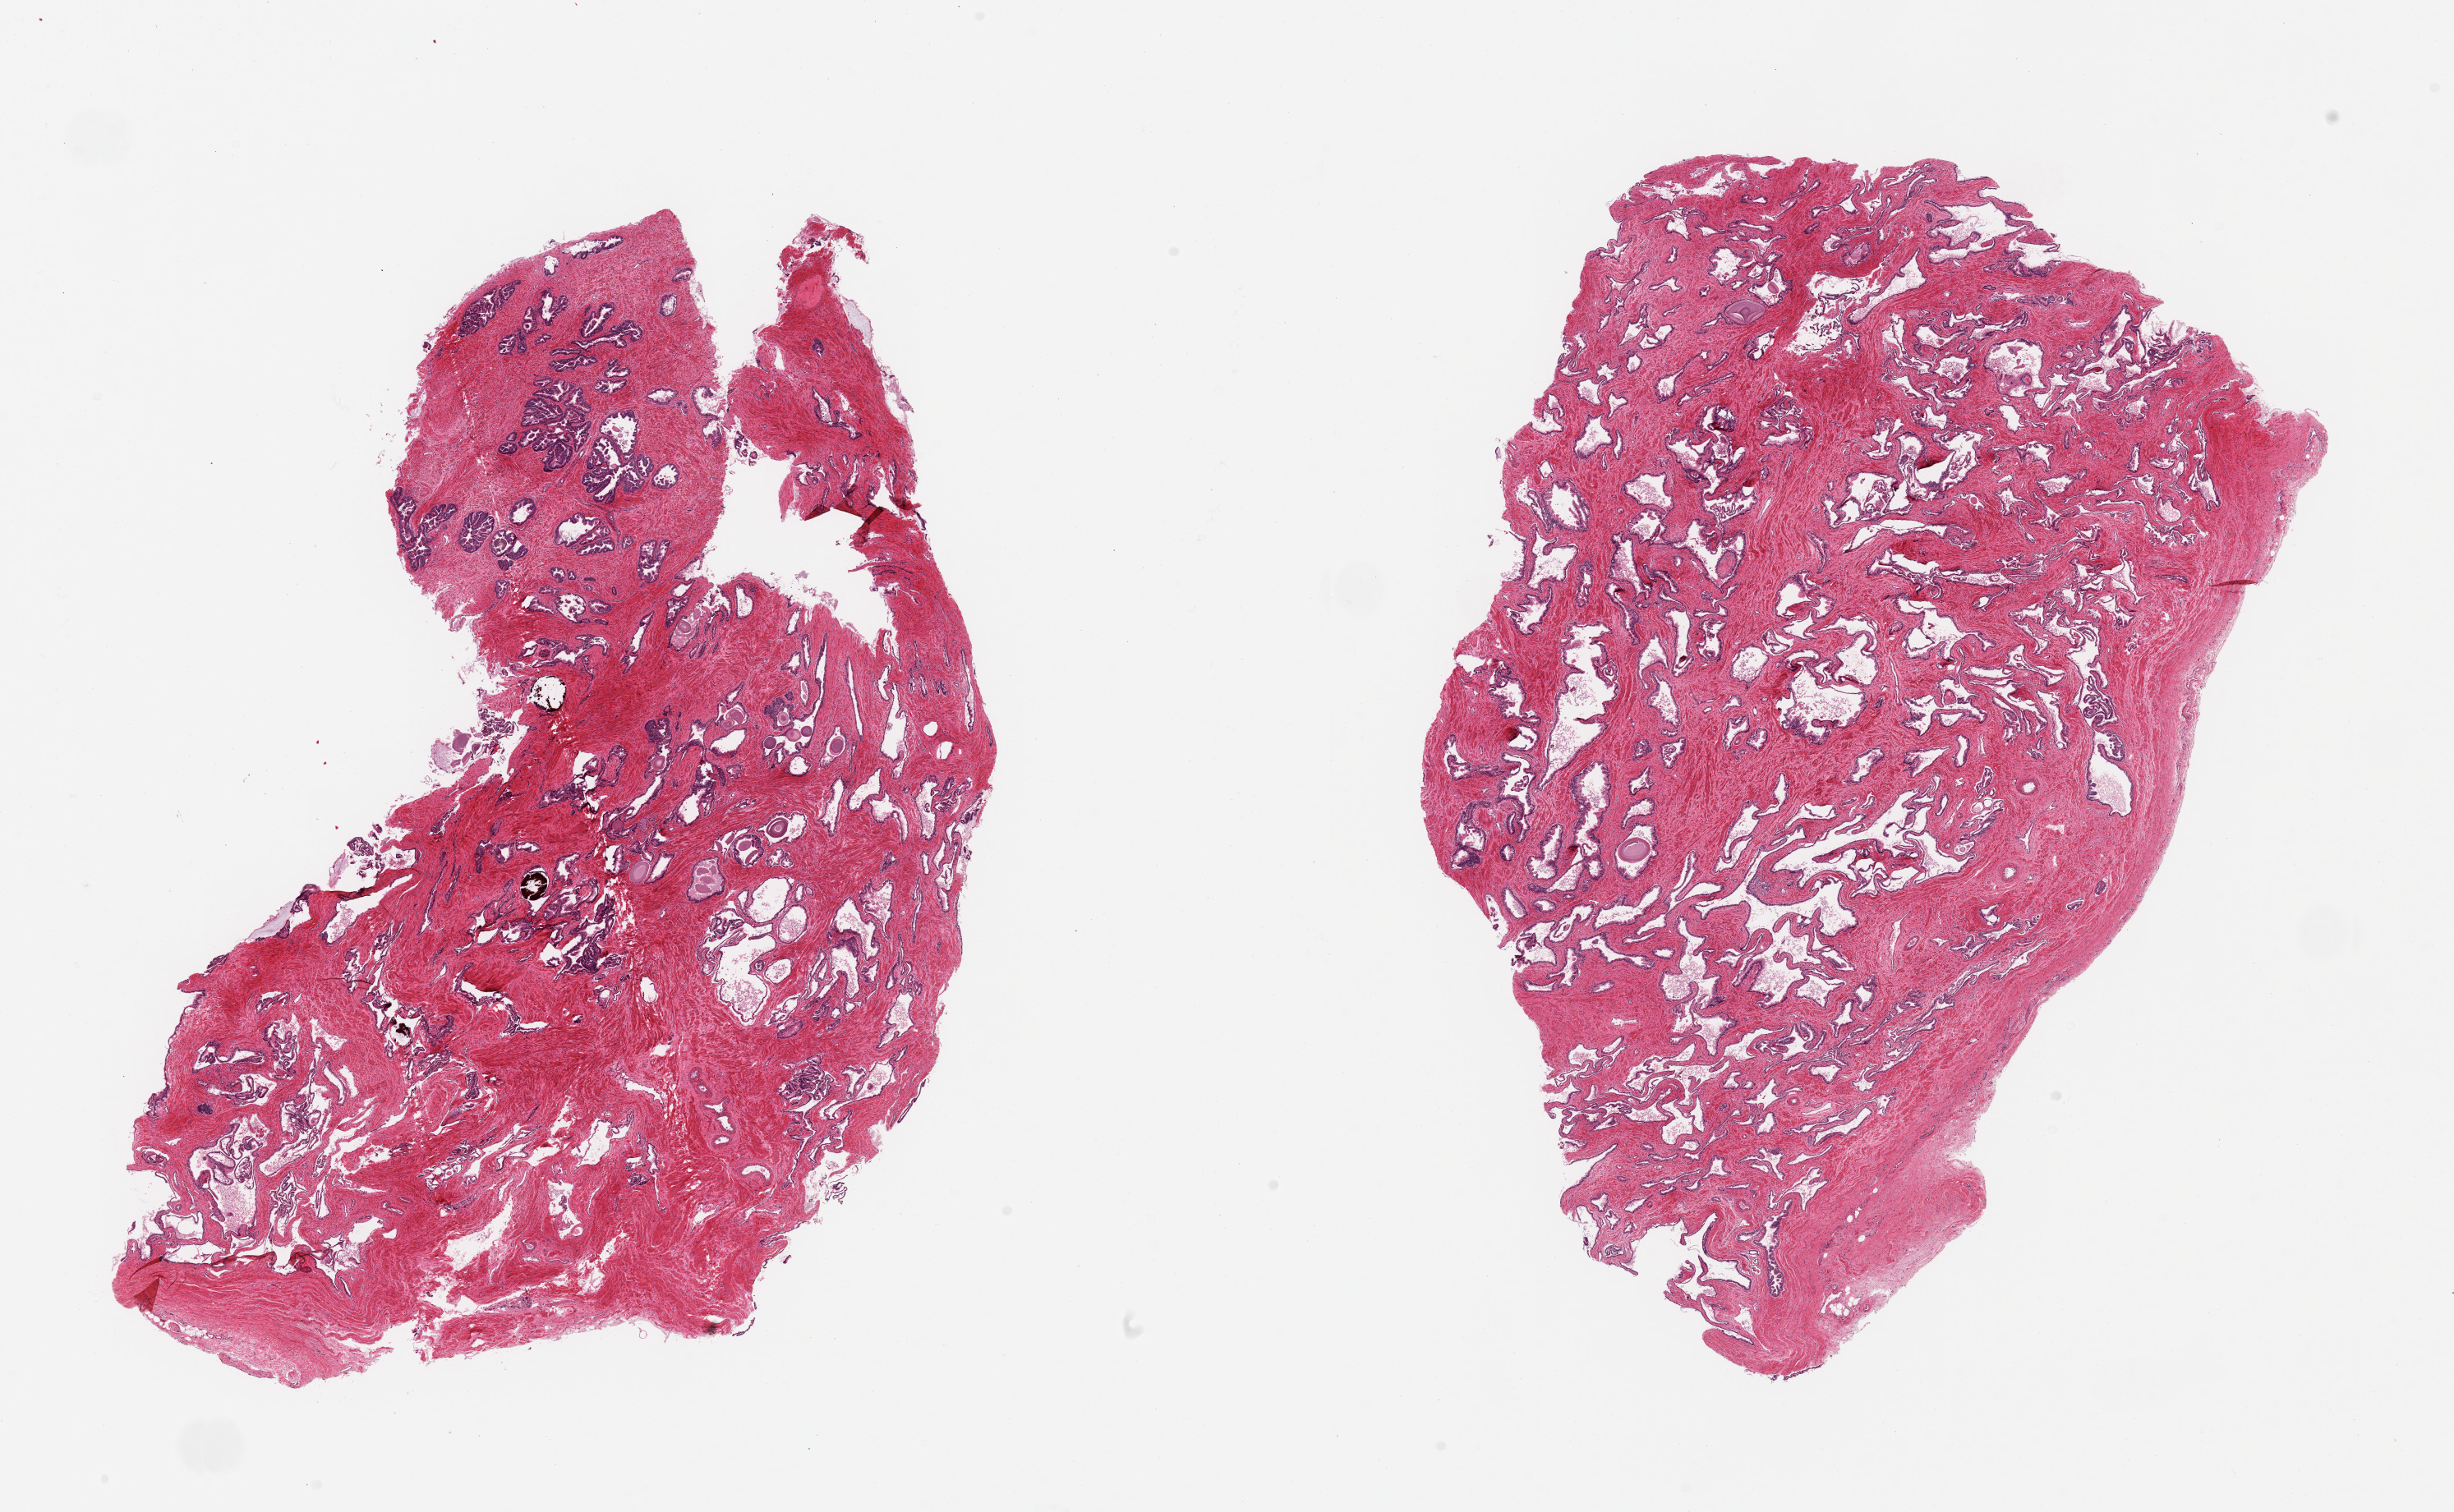
Haematoxylin and eosin whole-slide image — shown as a low-resolution overview of the whole scanned area (about 23.6 x 14.6 mm, acquisition: 20x scan), PAXgene-fixed paraffin-embedded (PFPE) section, sampled site (target tissue): prostate, donor tissue sample. Donor sex: male.
Reviewer comment on this tissue sample: 2 pieces; fibromuscular stroma with glands and many corpora amylacea.